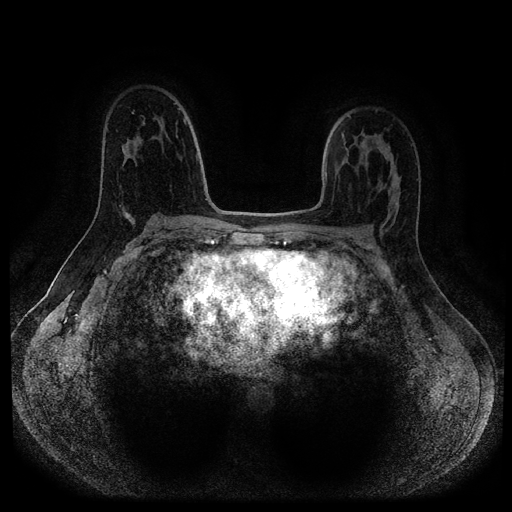
Breast MRI (dynamic contrast-enhanced, multi-phase), one axial slice. Slice 67 of 116 in the series (ordered by position). Dynamic contrast-enhanced series, time point 2 of 5 at this slice position (early post-contrast). 1.5 T. TE 2.7 ms, TR 5.4 ms. 2 mm slice thickness. 512 × 512 image matrix. Patient: female, 40 years.
Structures marked on this image (semi-automatically segmented with operator editing):
- breast lesion (labelled benign in the annotation): bounding box (x1, y1, x2, y2) in pixels: (118, 202, 136, 228)